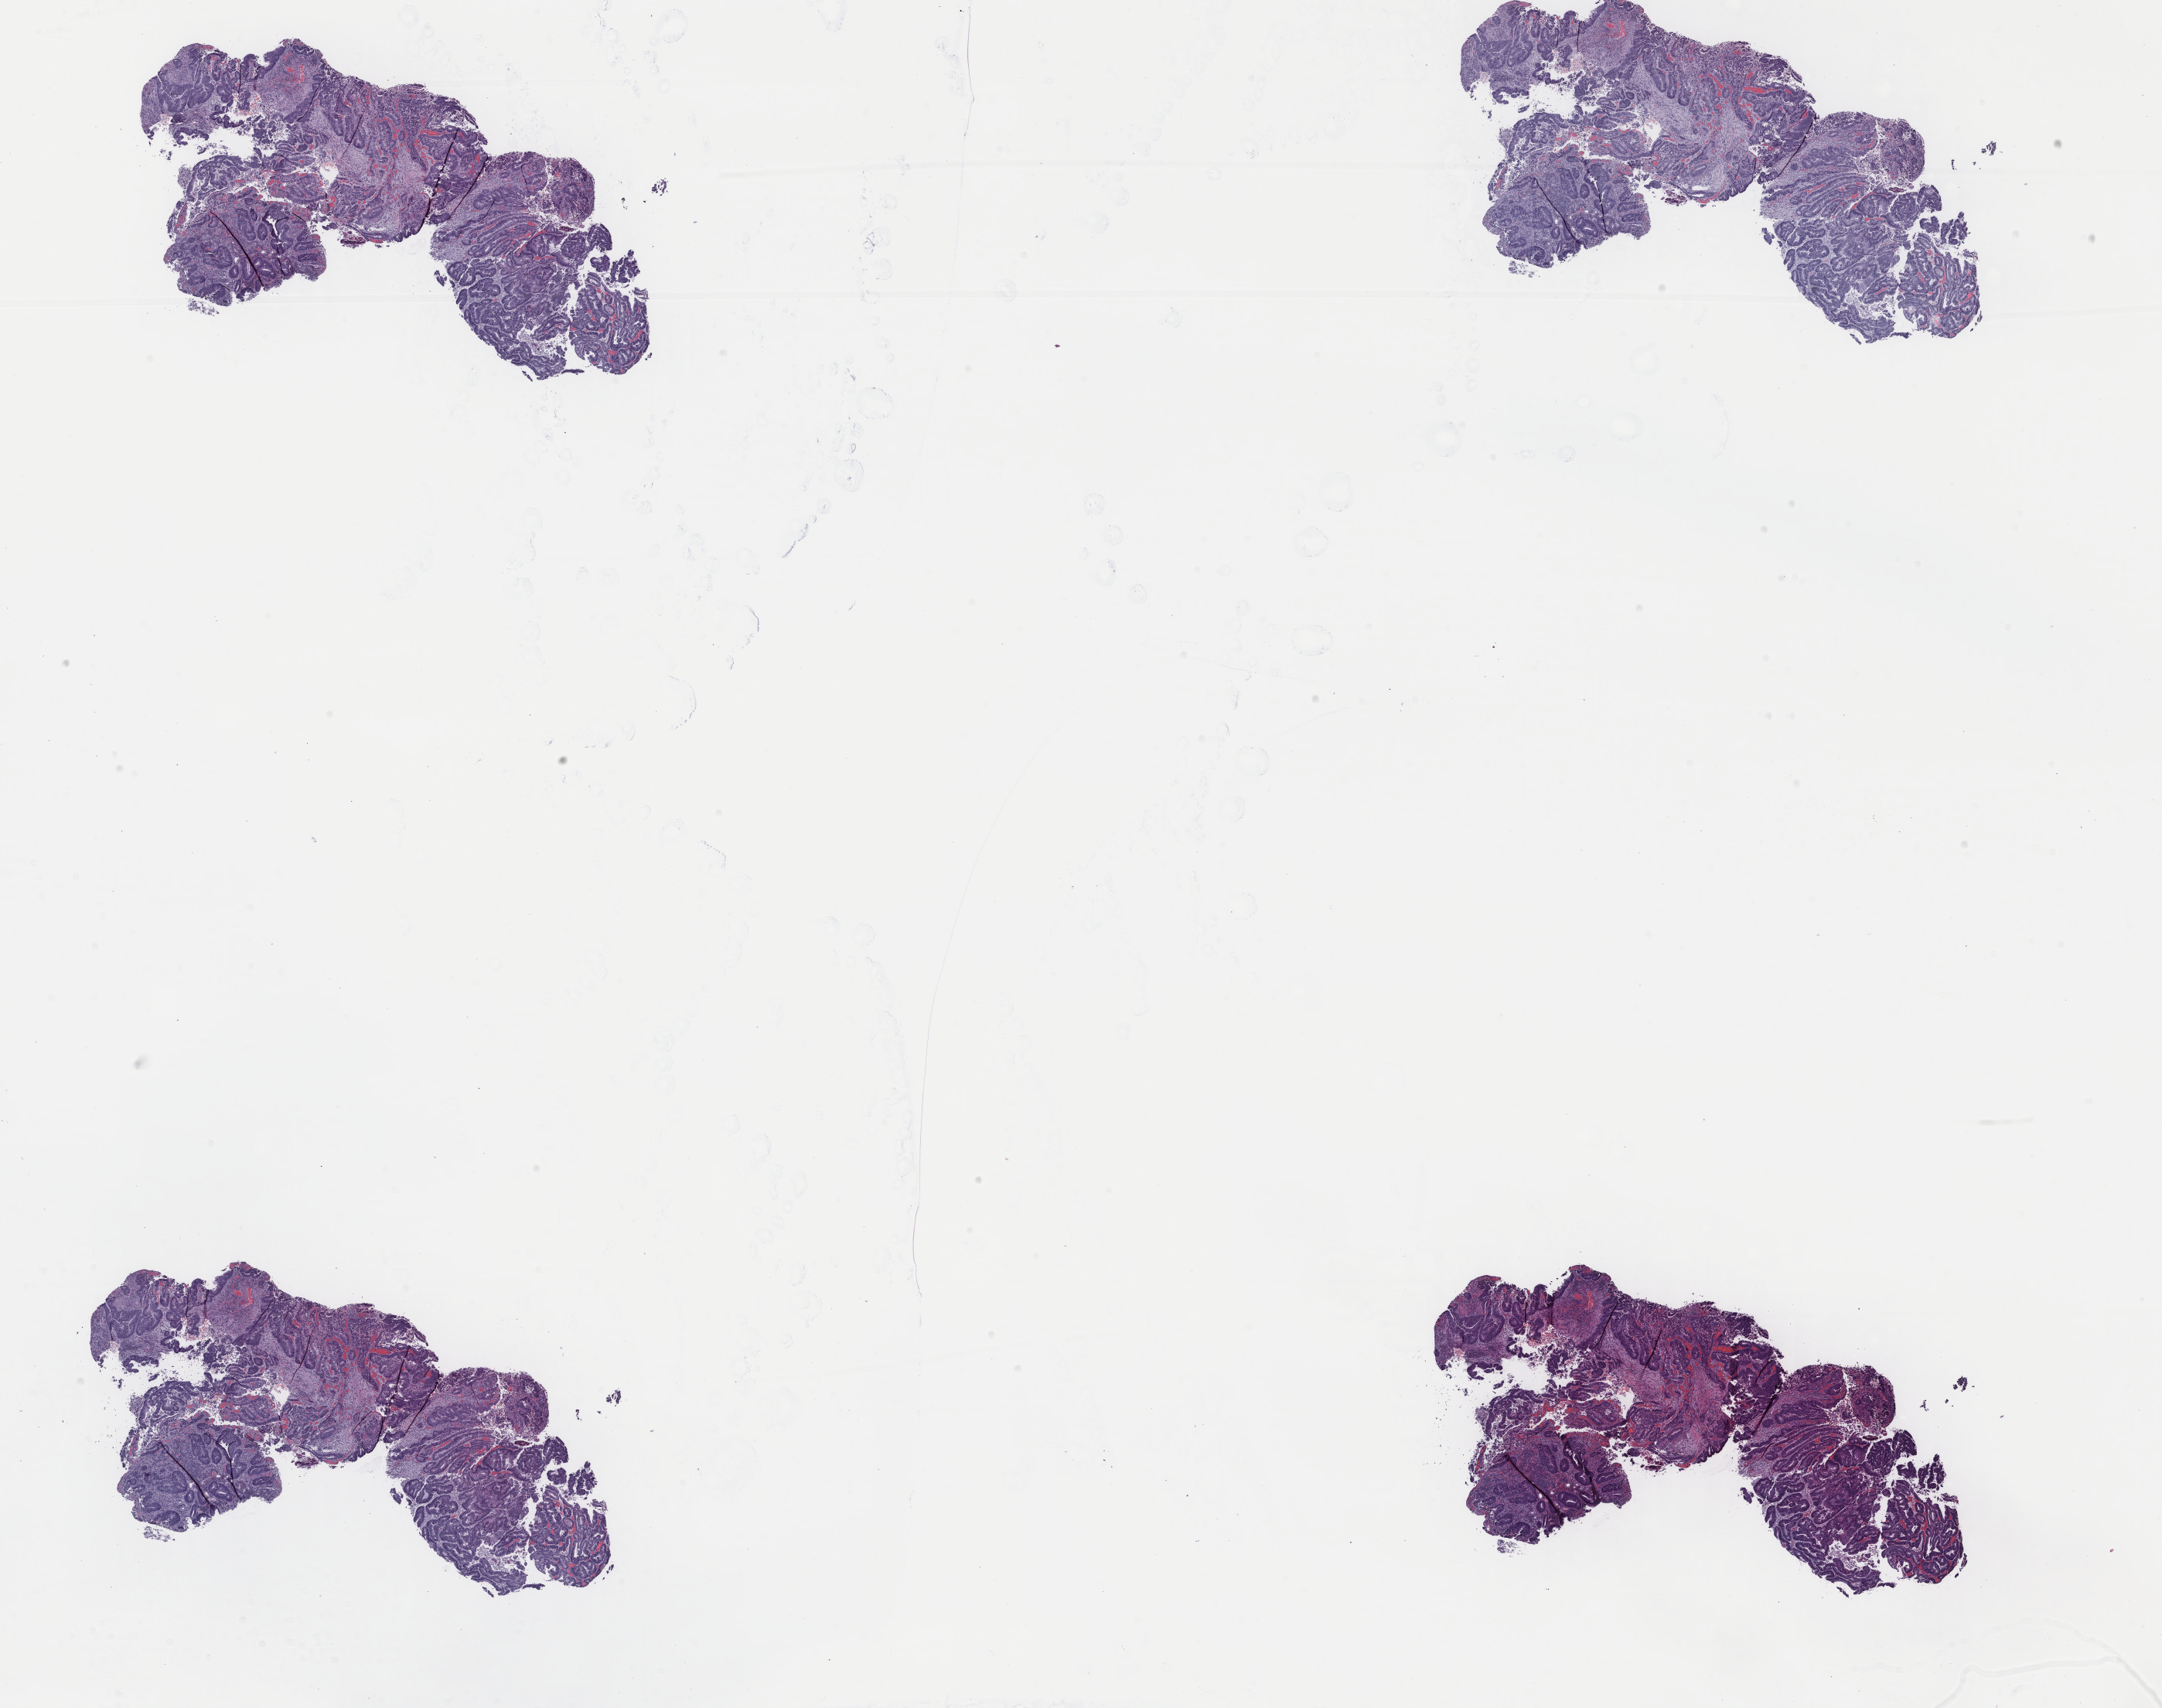
Whole-slide histology image, H&E, low-resolution overview of the scanned area, about 22.2 x 17.5 mm (acquisition: 40x scan), FFPE section, primary tumour sample from the rectum. Female, age 47 years at initial diagnosis.
Diagnosis: Adenocarcinoma, NOS. AJCC pathologic stage: IIA (7th edition). Lymph nodes positive (case pathology): 0 of 33 examined.